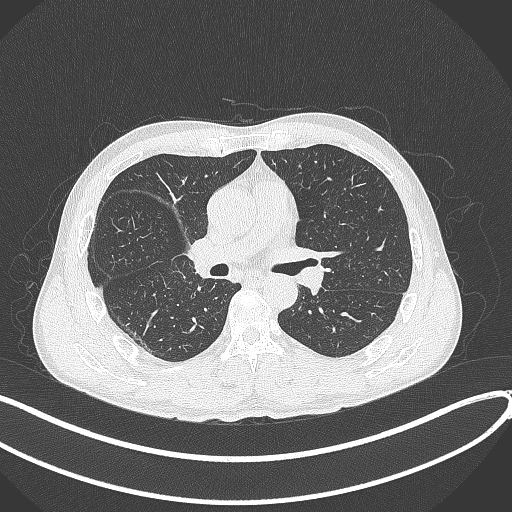
Chest CT, one axial slice. Slice 219 of 409 in the series (ordered by position). Reconstruction kernel B70f. 120 kVp. Lung window (W 1500 / L -600 HU). 1 mm slice thickness. 512 × 512 image matrix, field of view 400 × 400 mm. Patient: male, 53 years. From the clinical record (not read from this slice): clinical TNM (as recorded): T1b N0 M0.
Structures marked on this image (bounding box drawn by a radiologist):
- lung tumour (recorded histology: squamous cell carcinoma): bounding box [x1, y1, x2, y2] px = [187, 236, 217, 278]